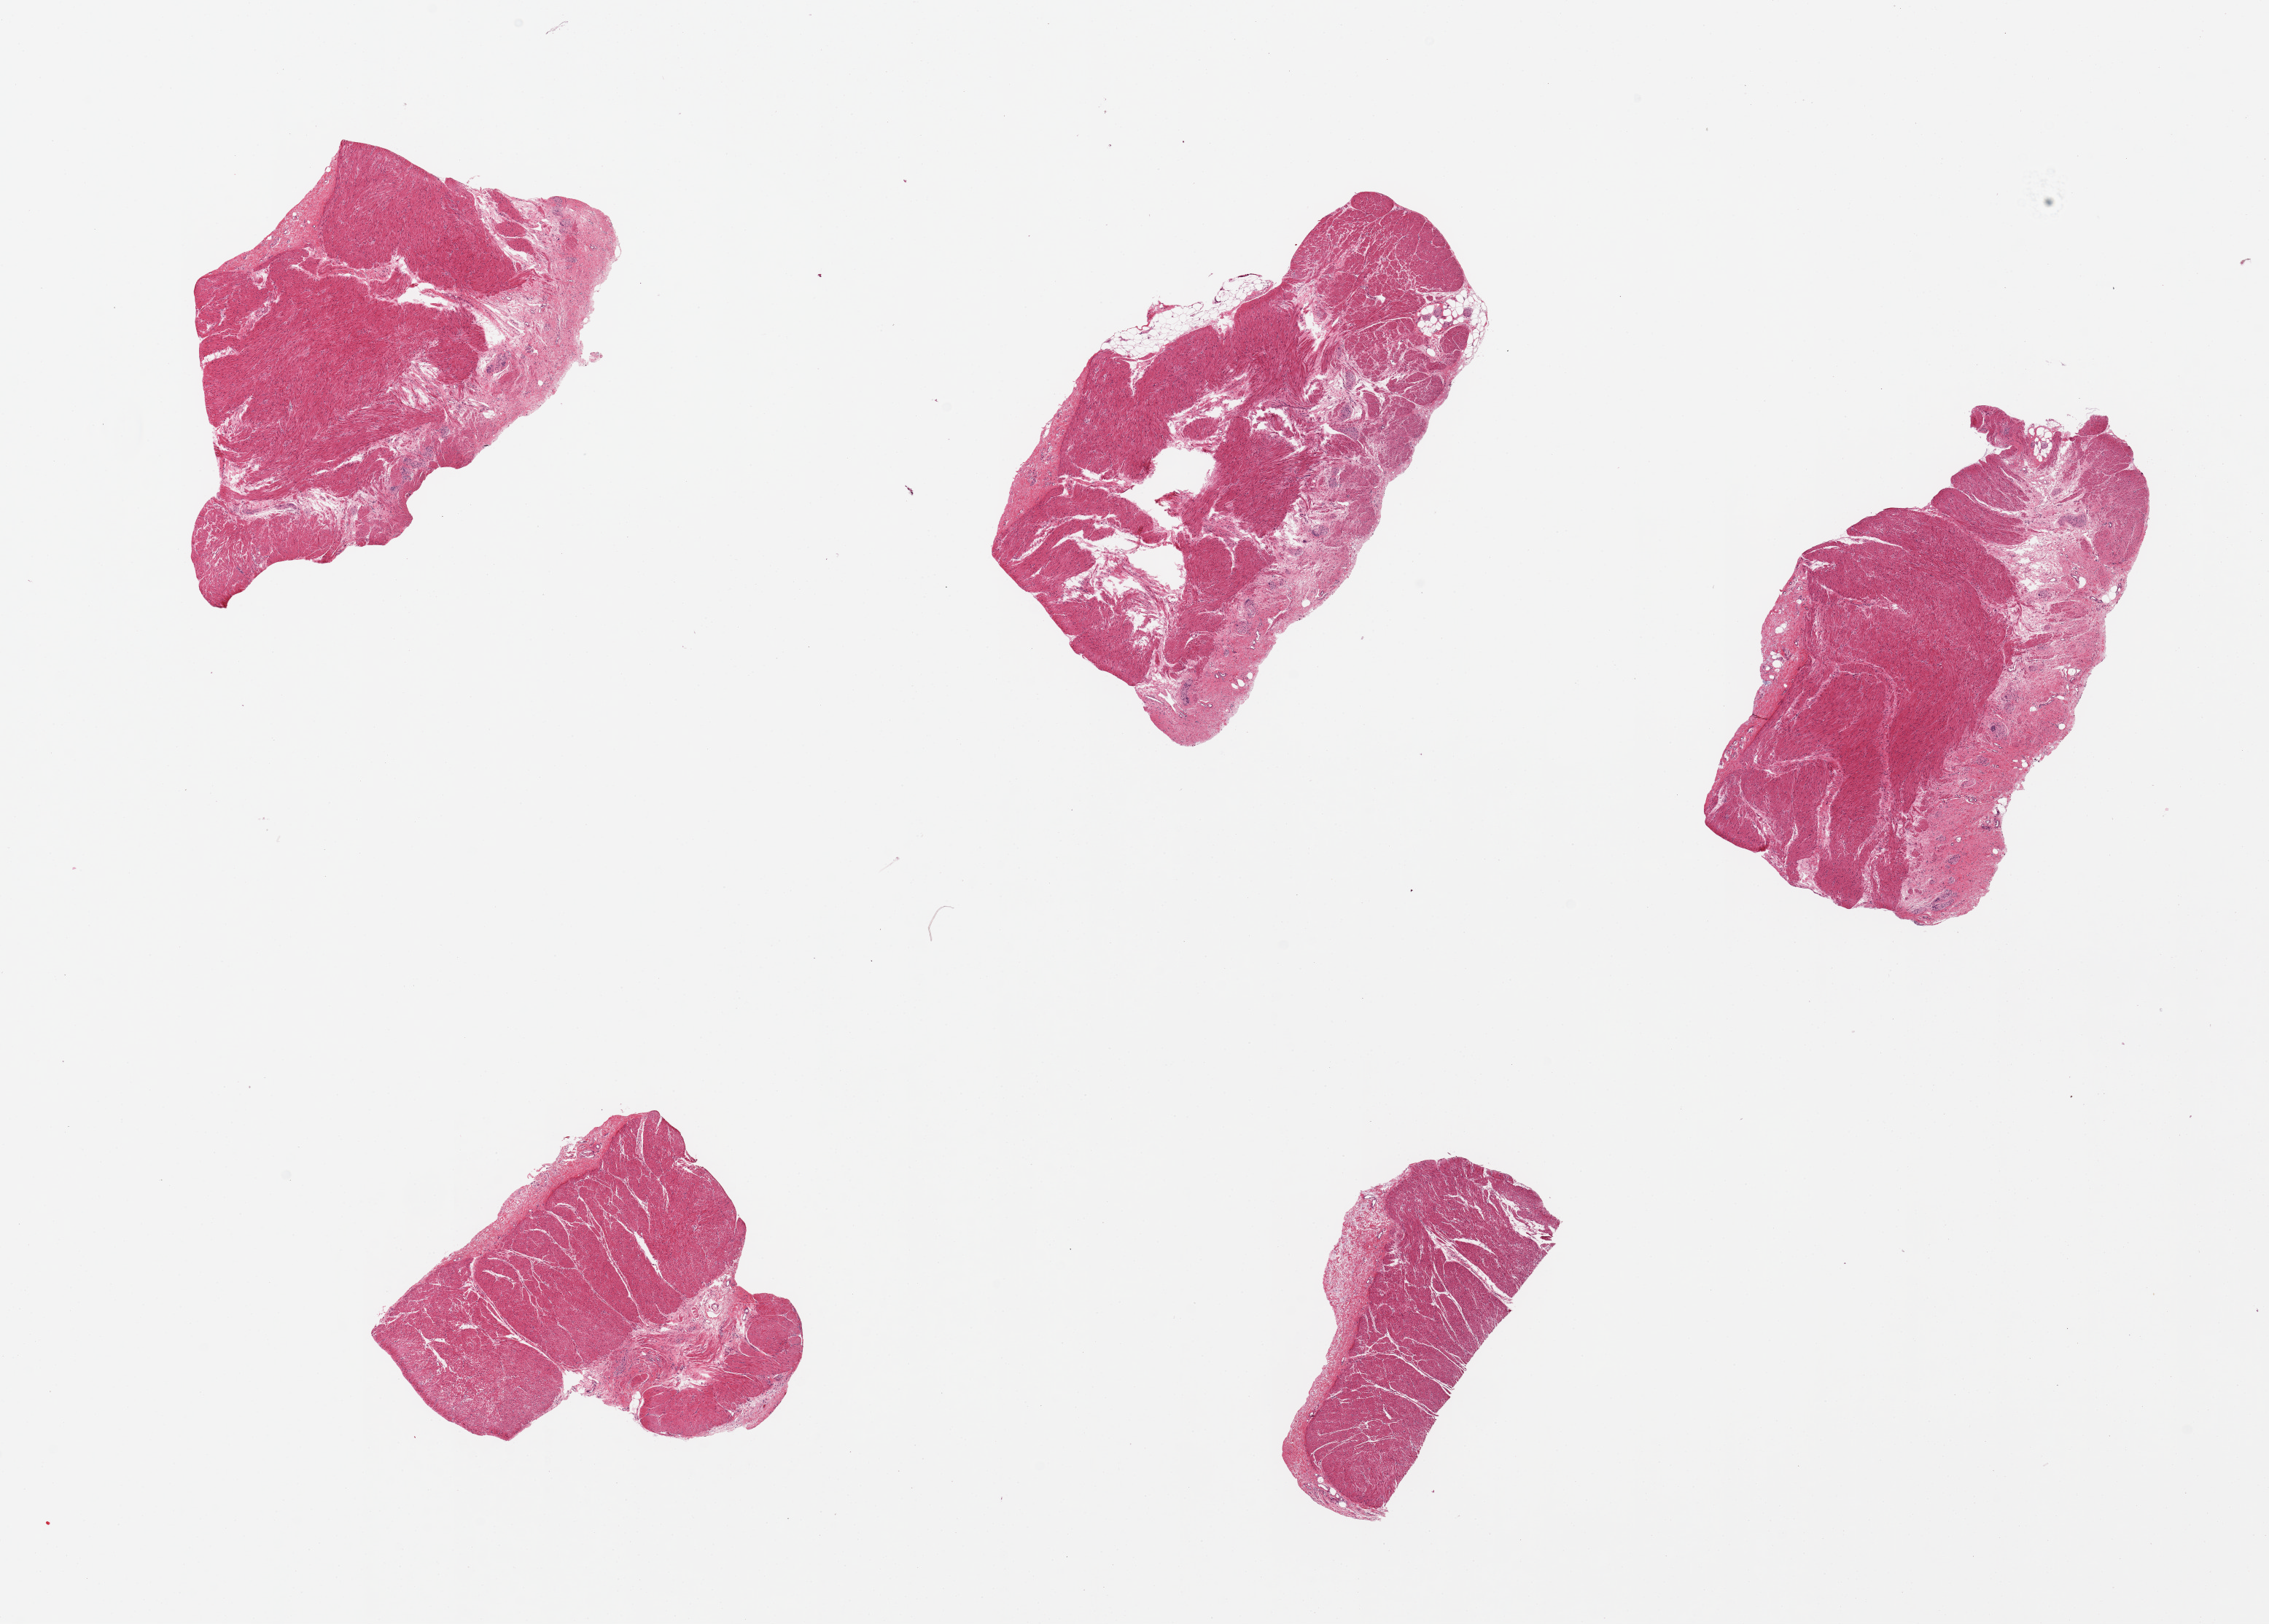
Digitized haematoxylin and eosin-stained section, low-resolution overview of the scanned area, about 24.6 x 17.6 mm (acquisition: 20x scan); PAXgene-fixed, paraffin-embedded tissue; section of sigmoid colon (target tissue); tissue donor sample. Female donor.
Review note (as recorded): 5 pieces, predominantly muscularis, focal connective tissue, good specimens.